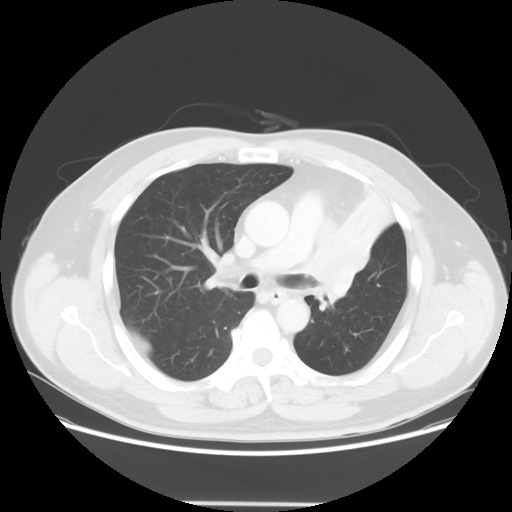
Chest CT, one axial slice. Position 38 of 62 along the scan axis. 120 kVp. Lung window (W 1500 / L -600 HU). 5 mm slice thickness. 512 × 512 image matrix, field of view 403 × 403 mm. Patient: male, 49 years. From the clinical record (not read from this slice): clinical TNM (as recorded): T3 N3 M1c.
Structures marked on this image (bounding box drawn by a radiologist):
- lung tumour (recorded histology: squamous cell carcinoma): bounding box (x1, y1, x2, y2) in pixels: (309, 216, 378, 313)